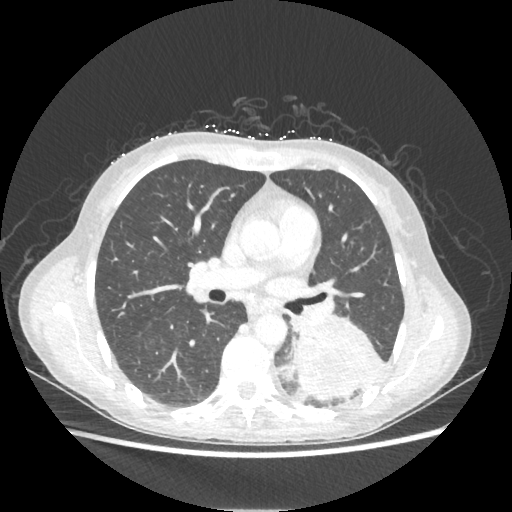
Chest CT, one axial slice. Position 123 of 221 along the scan axis. Reconstruction kernel STANDARD. Lung window (W 1500 / L -600 HU). 512 × 512 image matrix, field of view 360 × 360 mm. Female patient, age 53 years. From the clinical record (not read from this slice): clinical TNM (as recorded): T3 N0 M0.
Structures marked on this image (rectangle marked by the reading radiologist):
- lung tumour (recorded histology: adenocarcinoma): bounding box (x1, y1, x2, y2) in pixels: (295, 318, 380, 400)